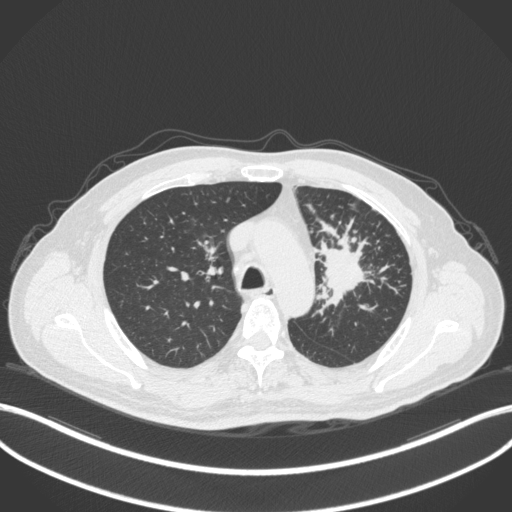
Chest CT, one axial slice. Position 255 of 386 along the scan axis. 120 kVp. Lung window (W 1500 / L -600 HU). 1 mm slice thickness. 512 × 512 image matrix, field of view 400 × 400 mm. Patient: male, 69 years. Case-level facts recorded for this patient, not image findings: clinical TNM (as recorded): T2a N2 M0.
Annotated regions visible in this slice (rectangle marked by the reading radiologist):
- lung tumour (recorded histology: adenocarcinoma): bounding box <315,239,376,308> (left, top, right, bottom; pixels)